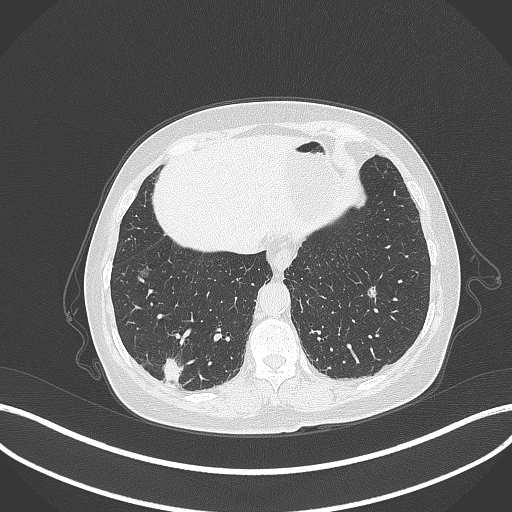
Chest CT, one axial slice. Position 64 of 333 along the scan axis. Reconstruction kernel B70f. 120 kVp. Lung window (W 1500 / L -600 HU). 512 × 512 image matrix, field of view 400 × 400 mm. Patient: female, 69 years. From the clinical record (not read from this slice): clinical TNM (as recorded): T1b N0 M0.
Structures marked on this image (rectangle marked by the reading radiologist):
- lung tumour (recorded histology: adenocarcinoma): bounding box (x1, y1, x2, y2) in pixels: (160, 353, 186, 384)